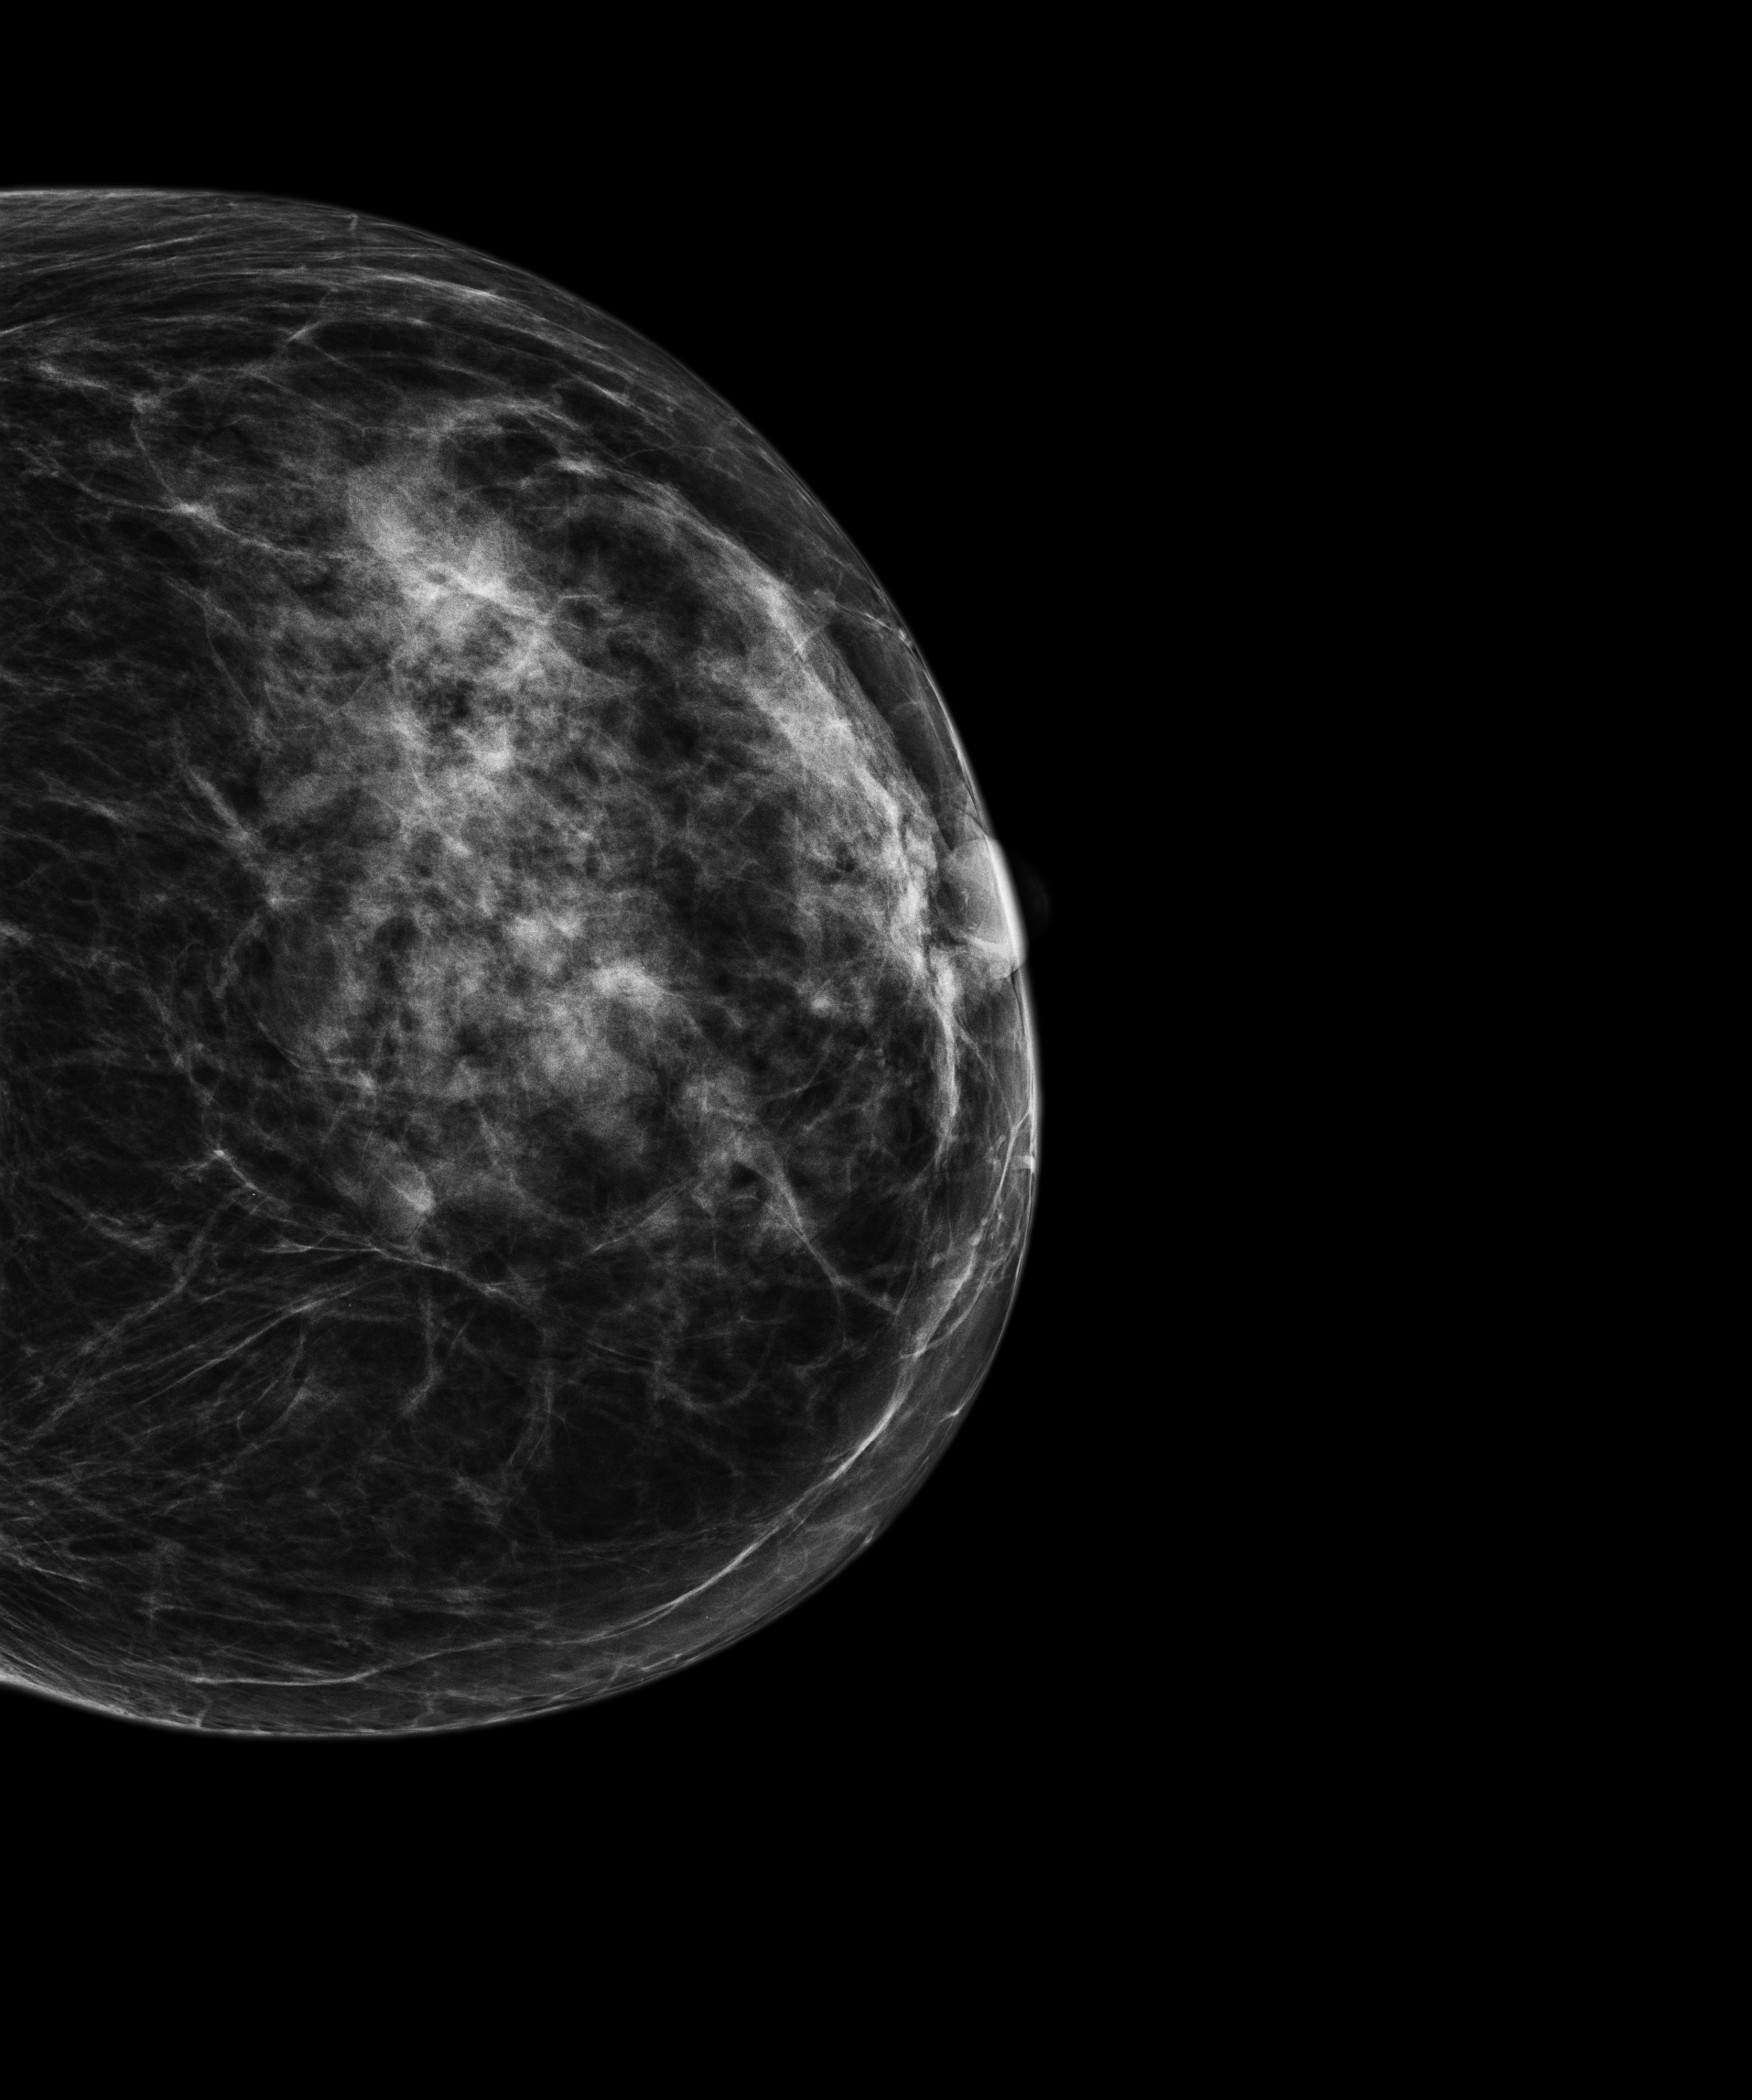
Digital mammogram (FFDM); left breast; cranio-caudal projection; screening examination; compressed breast thickness 36 mm; system: Senographe Essential ADS_56.21.3. Patient: female, 56 years.
BI-RADS breast density category at the screening exam (both breasts, scale 1–4): 3. Final BI-RADS category for the screening round (tomosynthesis exam, both breasts): category 1. Recall: no recall after this screen.